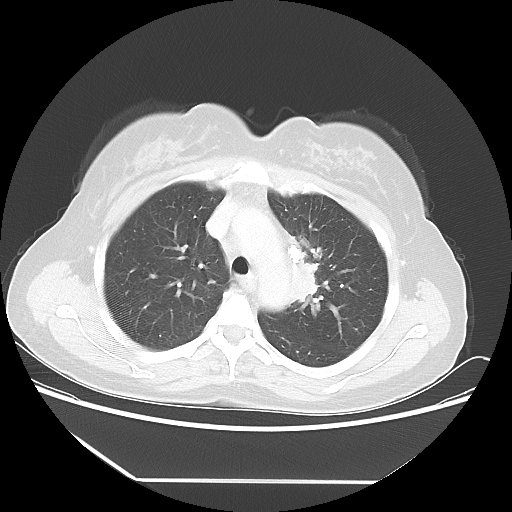
Chest CT, one axial slice. Slice 38 of 52 in the series (ordered by position). Reconstruction kernel LUNG. 100 kVp. Lung window (W 1500 / L -600 HU). 5 mm slice thickness. 512 × 512 image matrix. Female patient, age 50 years. From the clinical record (not read from this slice): clinical TNM (as recorded): T2 N3 M0.
Outlined on this slice (bounding box drawn by a radiologist):
- lung tumour (recorded histology: adenocarcinoma): bounding box (x1, y1, x2, y2) in pixels: (276, 226, 327, 324)